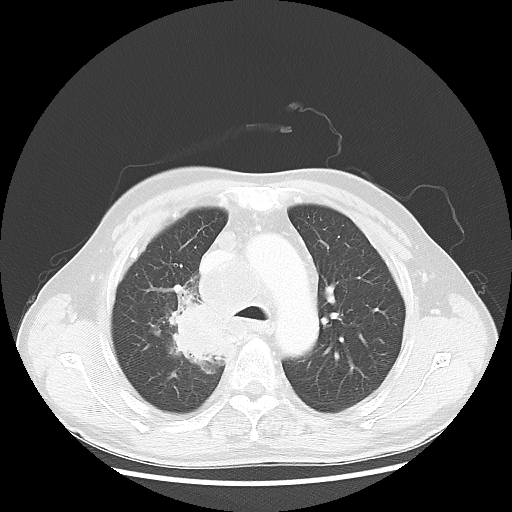
Chest CT, one axial slice; slice 41 of 60 in the series (ordered by position); lung window (W 1500 / L -600 HU); 512 × 512 image matrix. Patient: male, 64 years. Case-level facts recorded for this patient, not image findings: clinical TNM (as recorded): T3 N3 M0; histopathological grade: G3.
Annotated regions visible in this slice (bounding box drawn by a radiologist):
- lung tumour (recorded histology: small cell carcinoma): bounding box <172,299,235,373> (left, top, right, bottom; pixels)